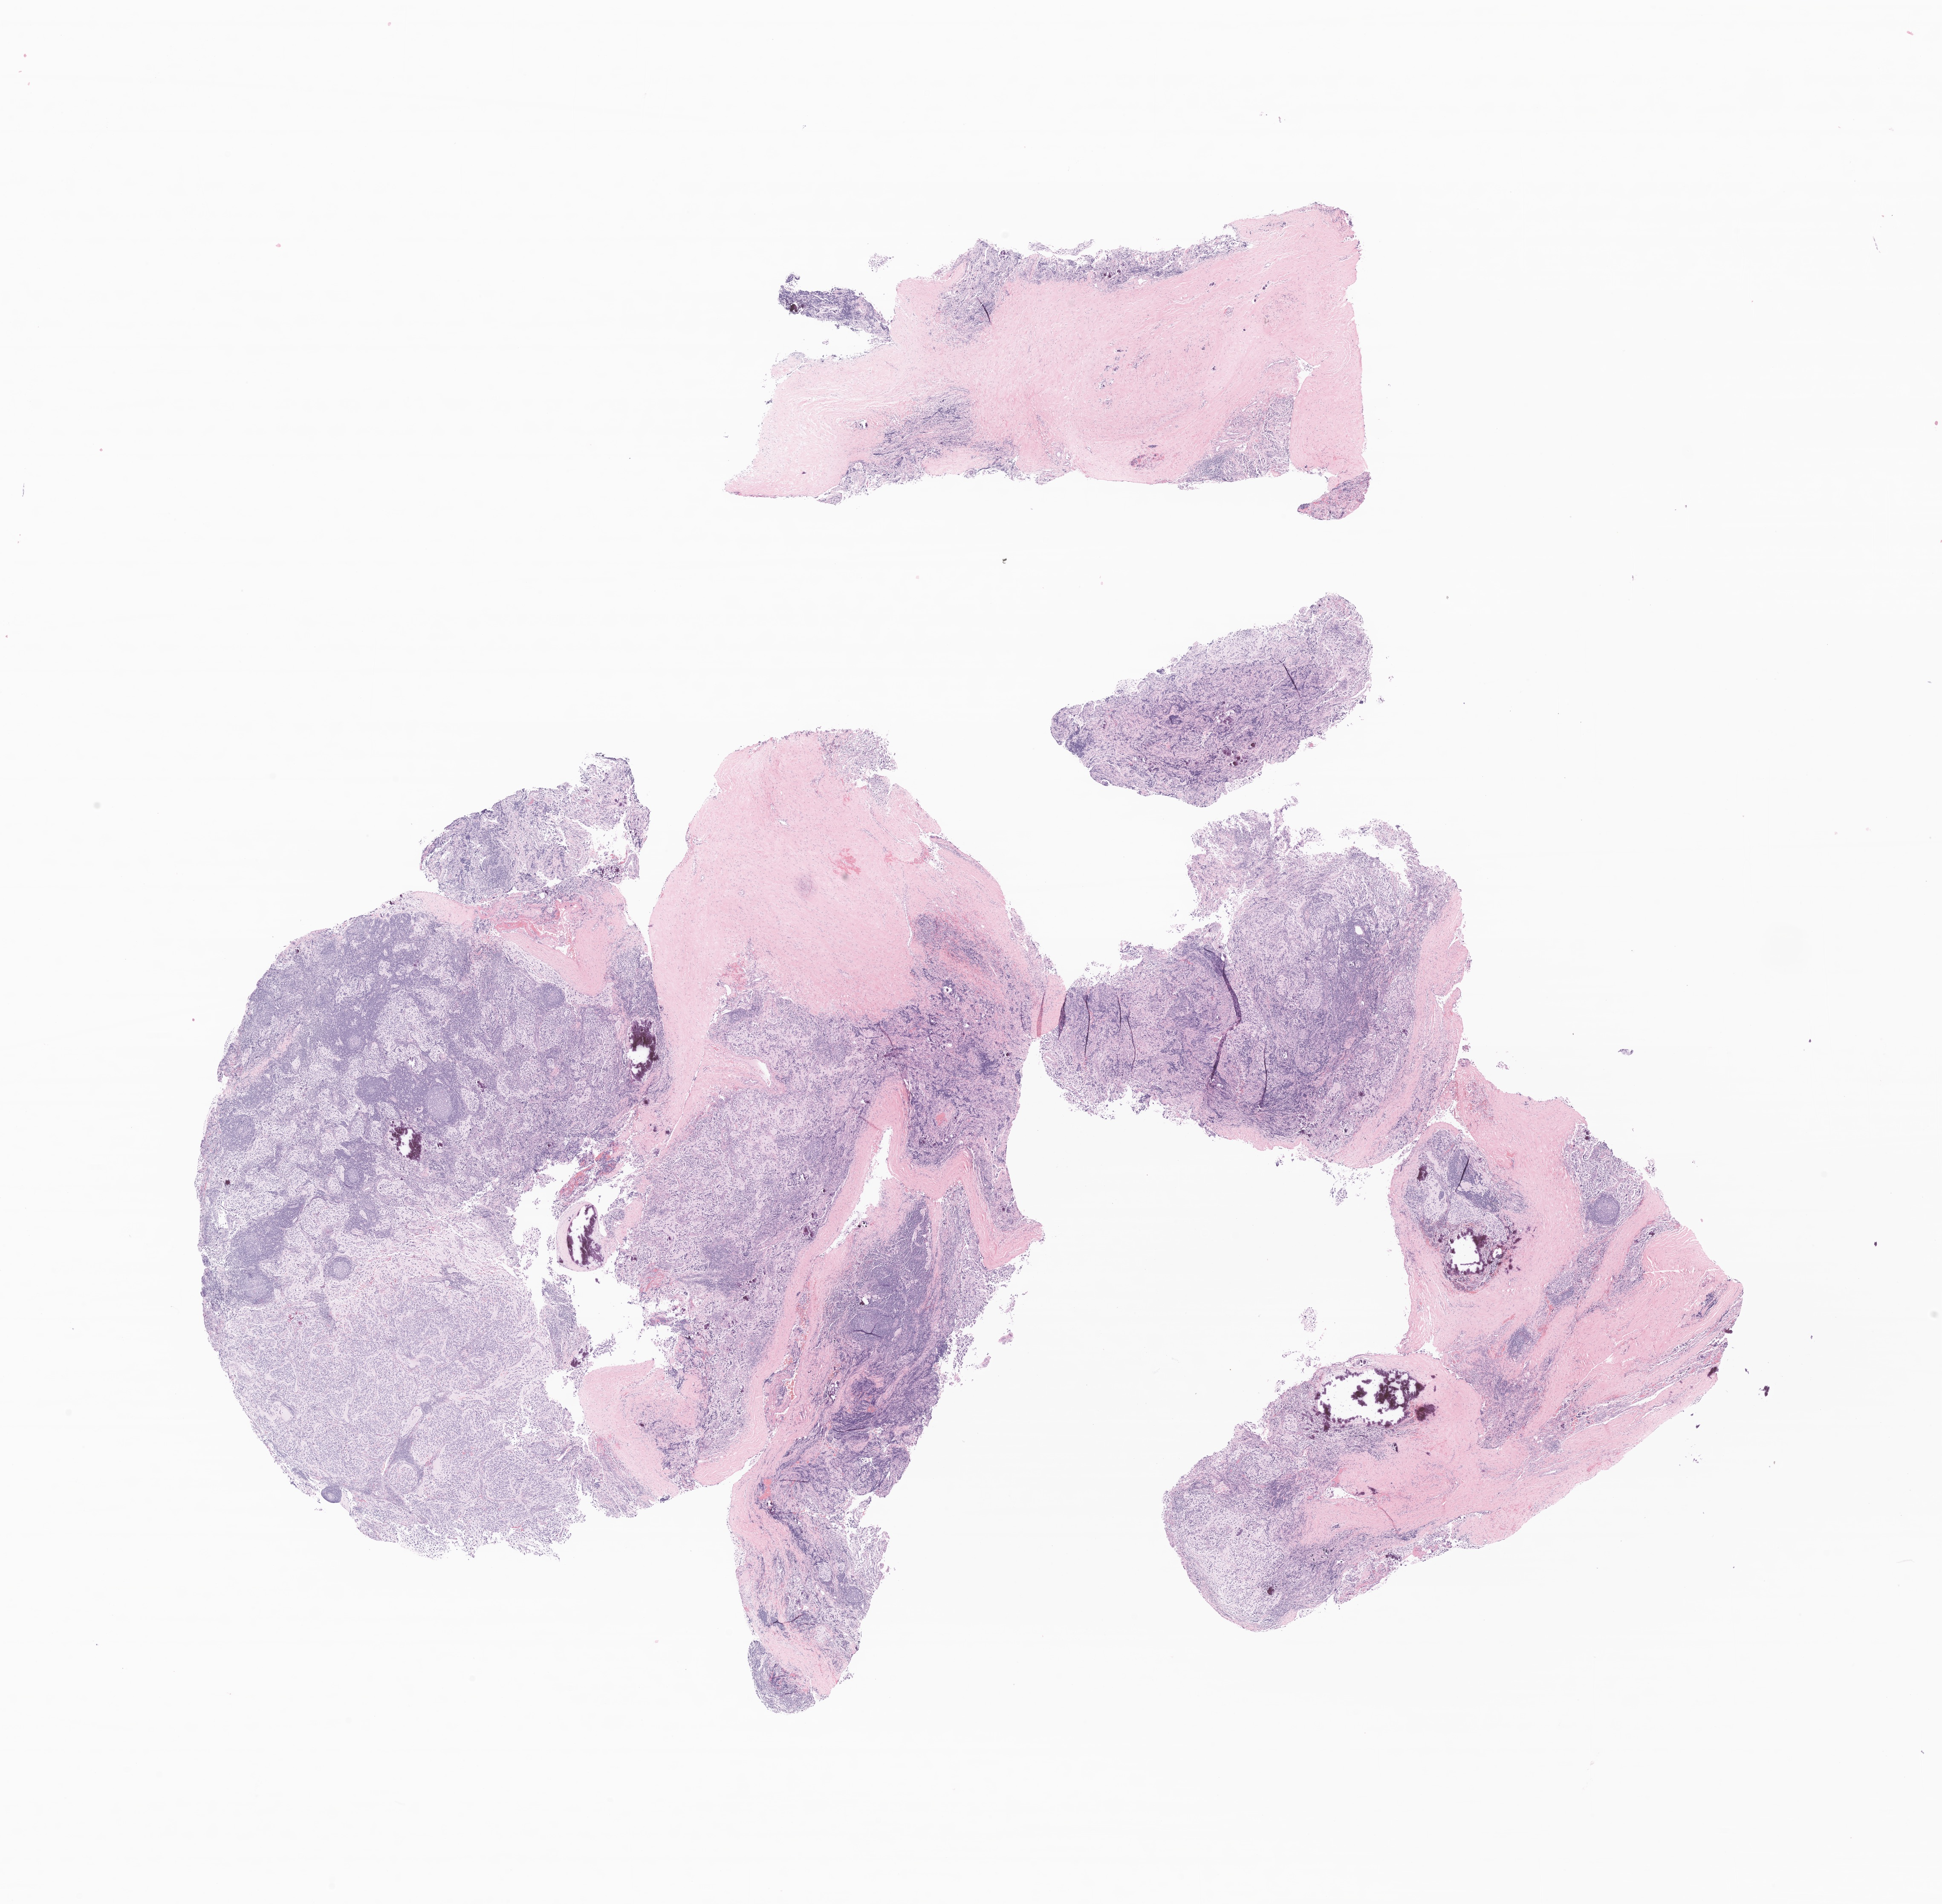
Hematoxylin and eosin (H&E) whole-slide image of tumor tissue from the adrenal gland — low-resolution overview of the scanned area, about 19.2 x 18.8 mm, formalin-fixed, paraffin-embedded (FFPE) tissue. Male patient, age 794 days (about 2.2 years).
Diagnosis: Neuroblastoma, NOS.